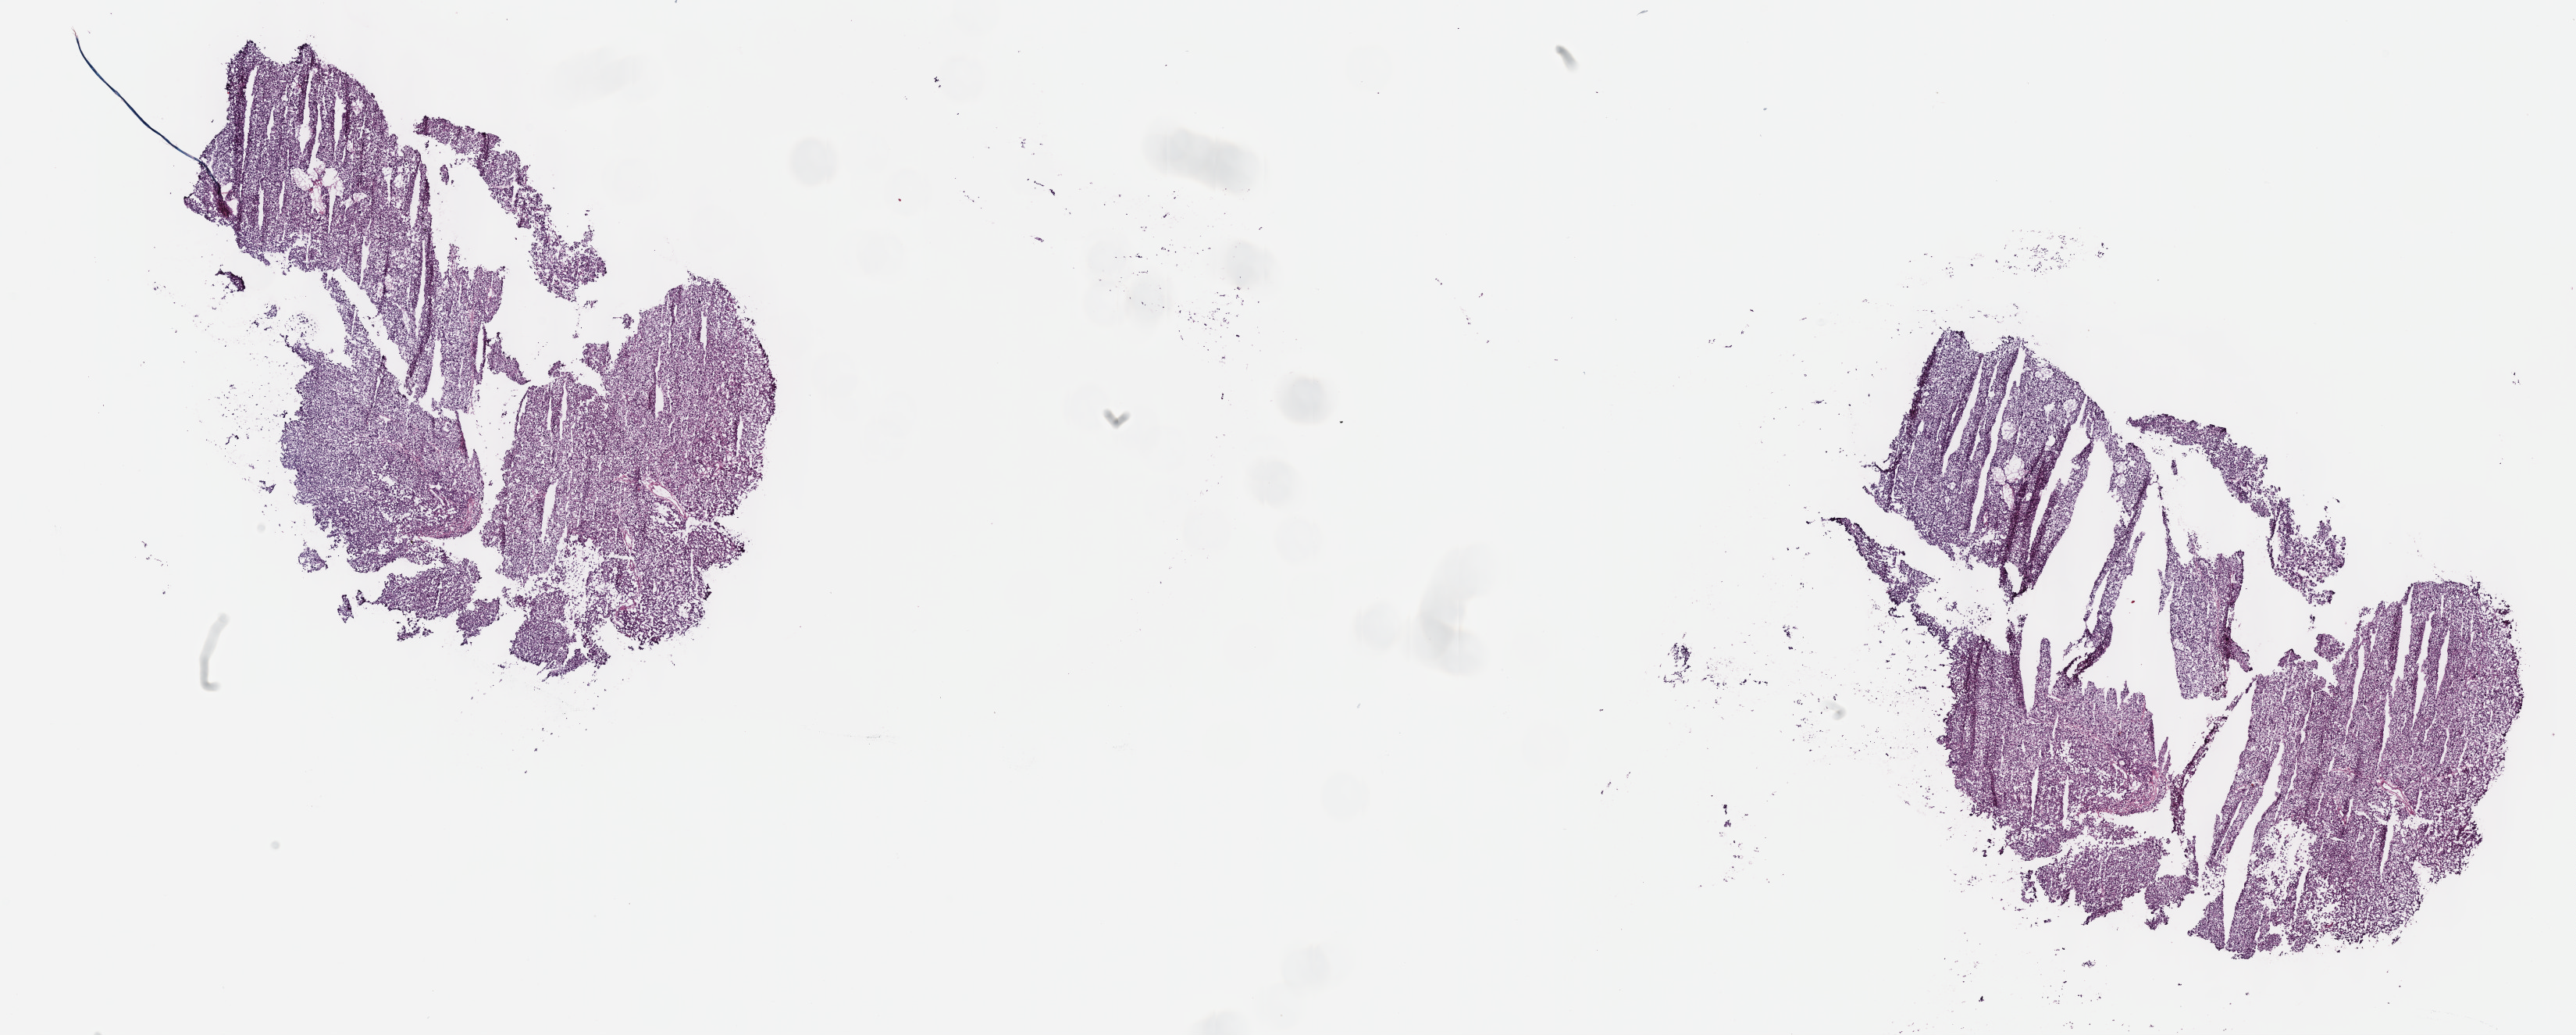
Digitized Hematoxylin and eosin (H&E) stained tissue section (whole slide), low-resolution overview of the scanned area, about 26.7 x 10.7 mm (slide scanned at 40x), frozen section from the top of the tissue portion, primary tumour sample from the liver. Patient: male, age at initial diagnosis 24 years. Histologic grade: G3 (poorly differentiated). Composition of this section per pathologist review: tumour cells 90%, tumour nuclei 95%, normal cells 0%, stromal cells 10%, necrosis 0%. Inflammatory infiltration, as recorded: lymphocyte infiltration 0%, monocyte infiltration 0%, neutrophil infiltration 0%.
Pathologic diagnosis: Hepatocellular carcinoma, NOS. AJCC pathologic stage: II (7th edition).